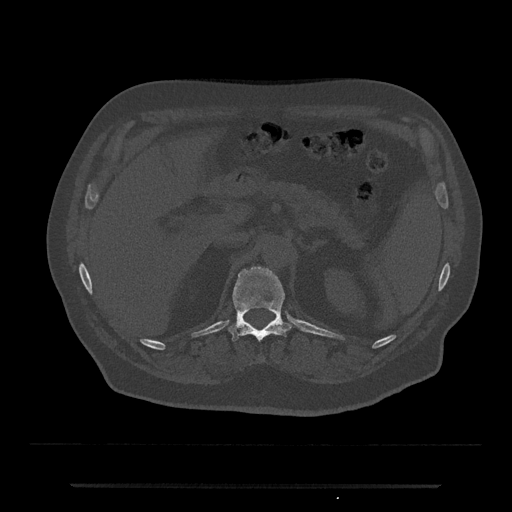
CT including the spine, one axial slice. Position 593 of 797 along the scan axis. 120 kVp. Bone window (W 1800 / L 400 HU). 0.5 mm slice thickness. 512 × 512 image matrix. Male patient, age 80 years. Case-level facts recorded for this patient, not image findings: primary cancer: prostate; vertebrae with lytic lesions (as recorded): L1, T11.
Annotated regions visible in this slice (semi-automatic segmentation, software-assisted and operator-edited):
- T12 vertebra: box from (x=228, y=266) to (x=291, y=342) px